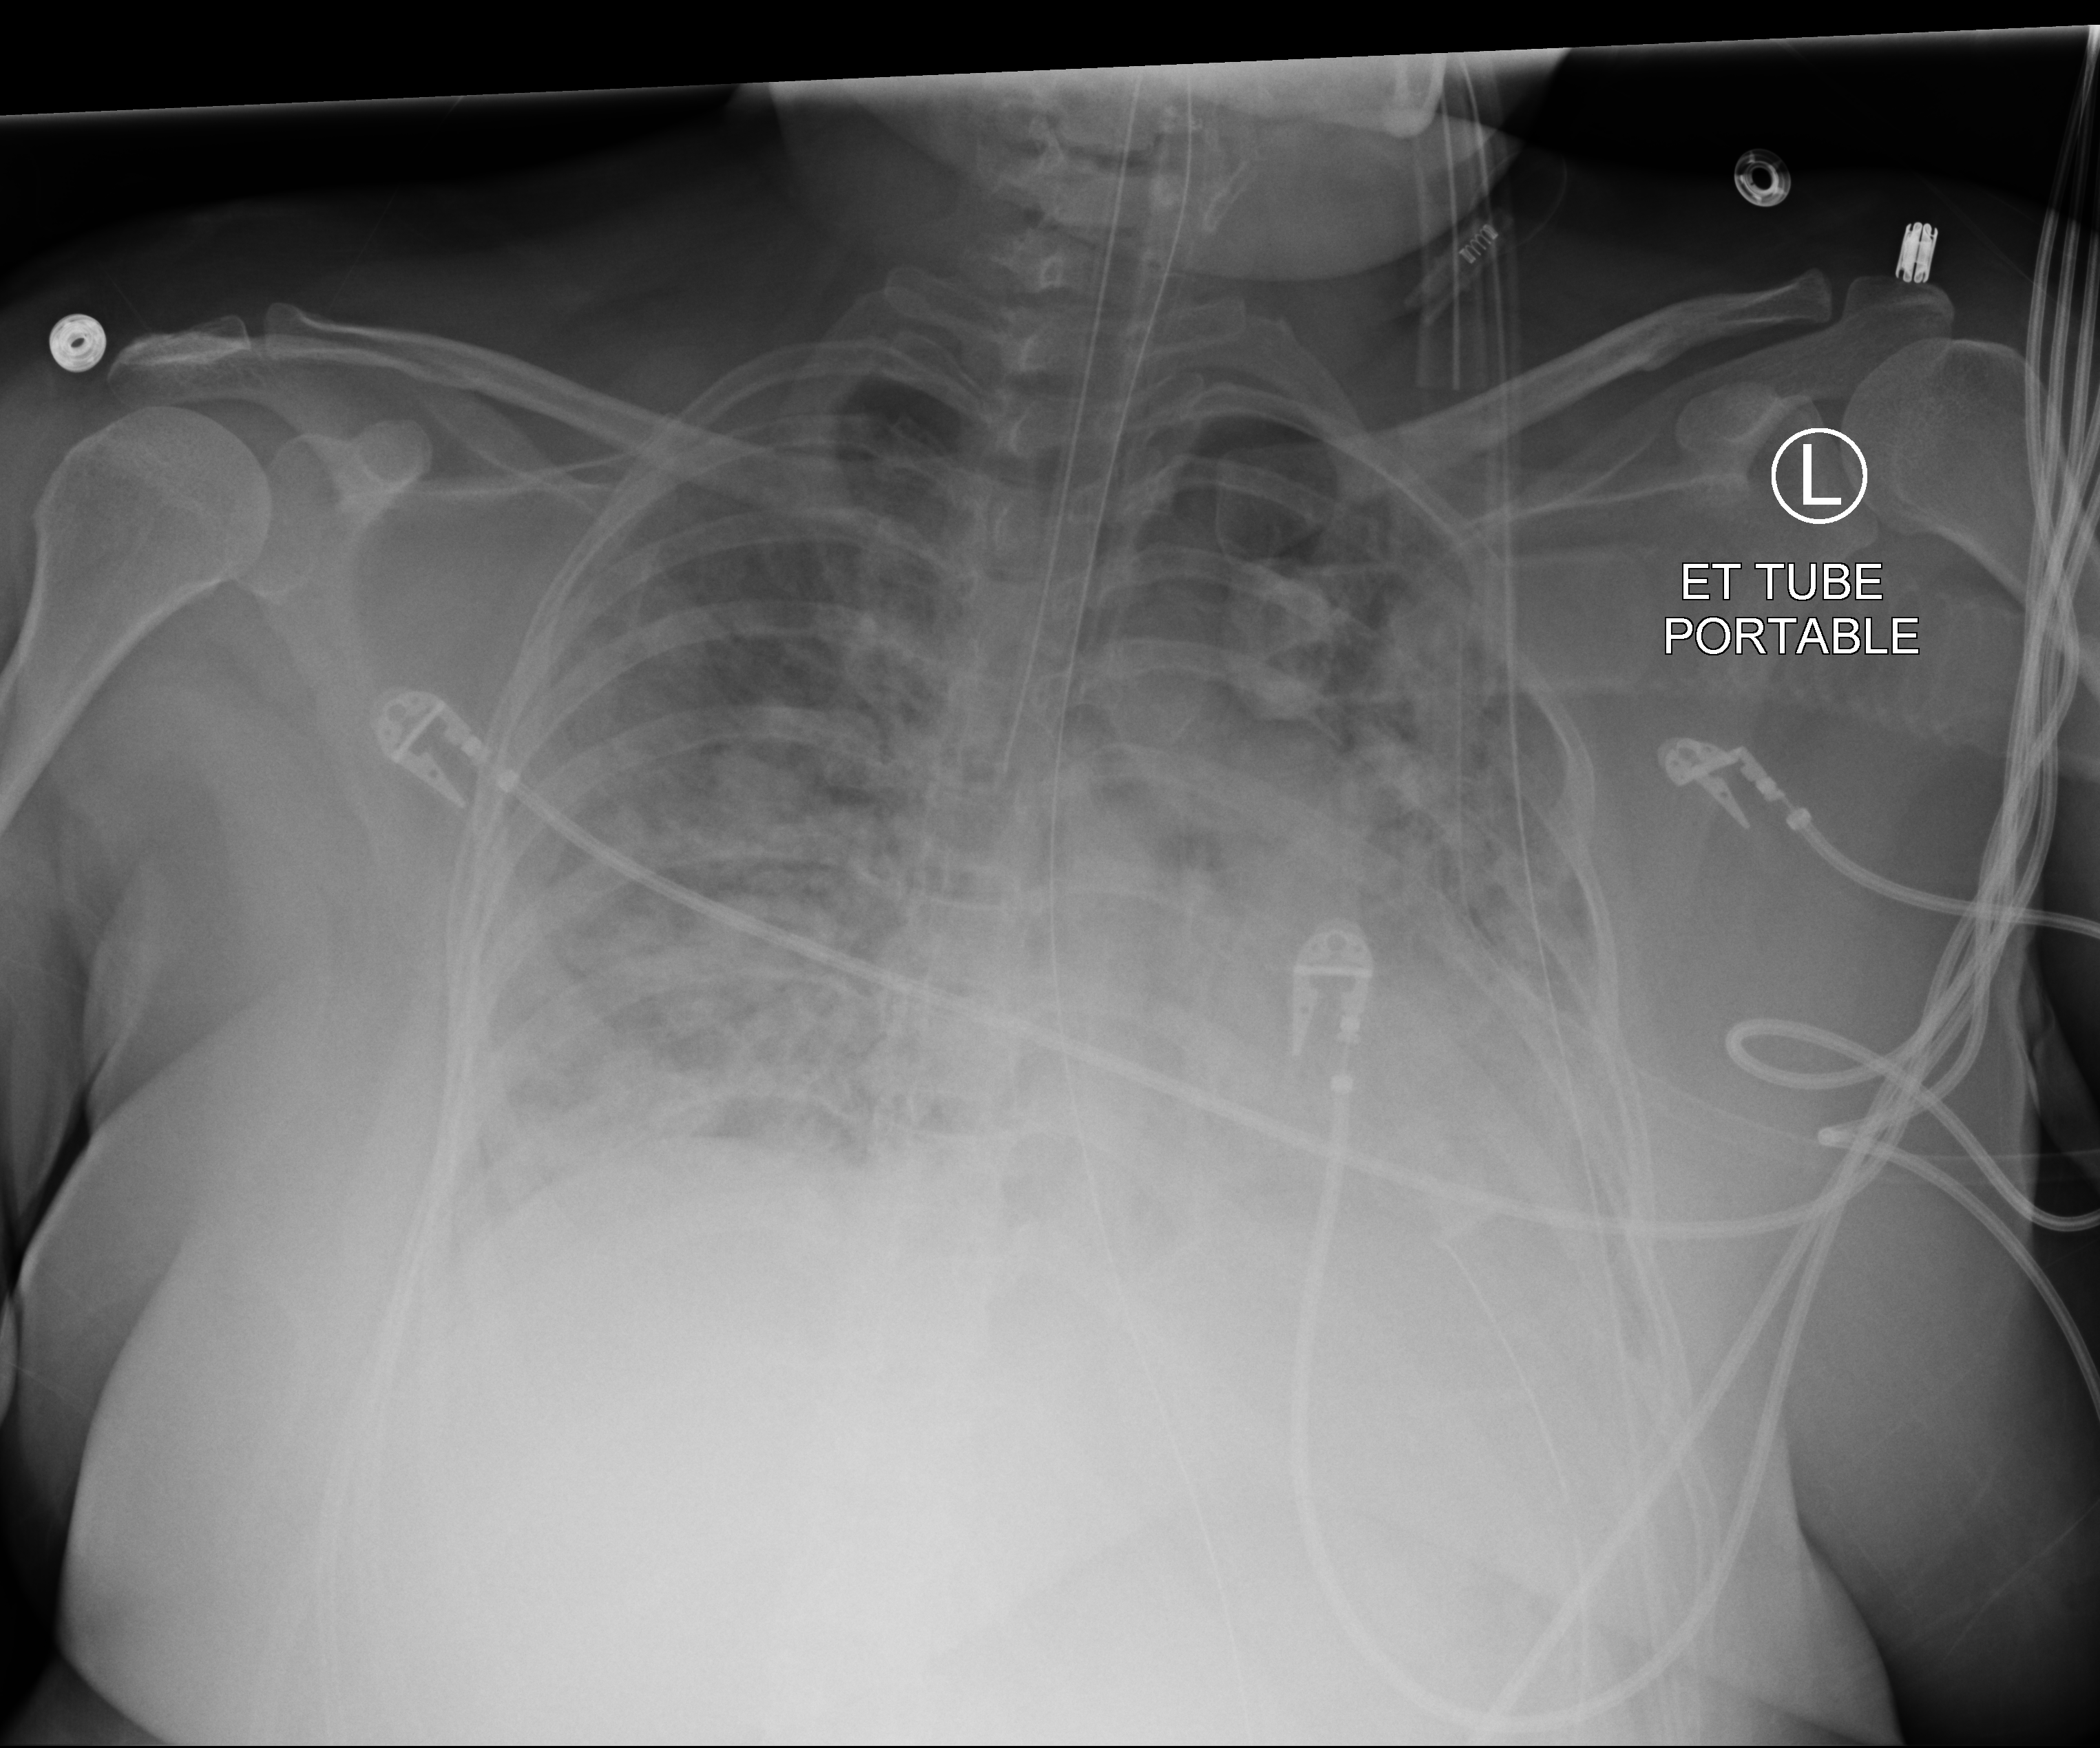
Portable chest radiograph, anteroposterior (AP) projection. Adult patient hospitalised with COVID-19, age 18–59 years.
Admission-level facts for this patient (not findings on this image; timing relative to this image not recorded): admitted to intensive care during this hospital stay: yes; length of hospital stay: 10 days.